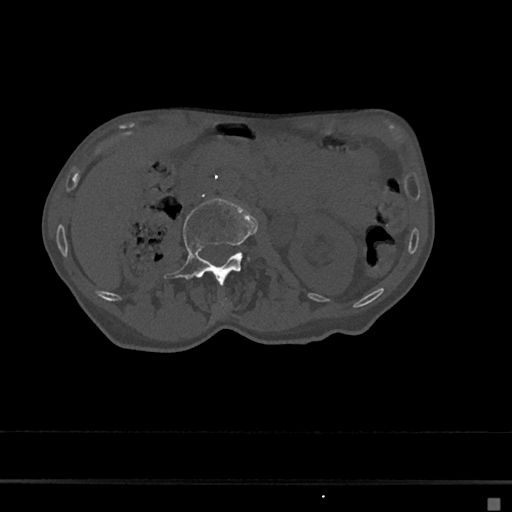
CT including the spine, one axial slice; position 14 of 797 along the scan axis; bone window (W 1800 / L 400 HU); 0.5 mm slice thickness; 512 × 512 image matrix. Patient: female, 68 years. From the clinical record (not read from this slice): primary cancer: renal.
Structures marked on this image (semi-automatically segmented with operator editing):
- L1 vertebra: bounding box <219,298,229,311> (left, top, right, bottom; pixels)
- L2 vertebra: <164,199,257,282>